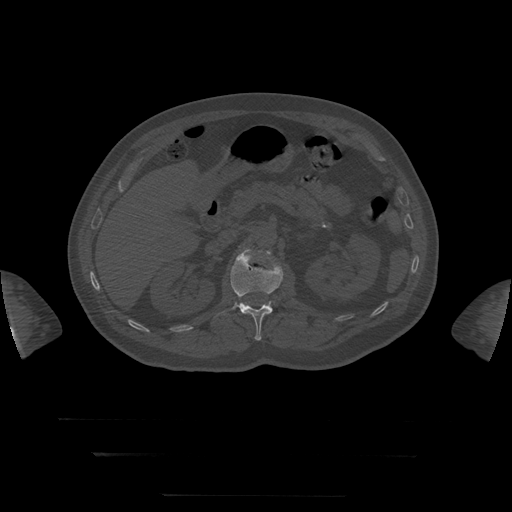
CT including the spine, one axial slice. Reconstruction kernel STANDARD. 120 kVp. Bone window (W 1800 / L 400 HU). 512 × 512 image matrix, field of view 510 × 510 mm. Patient age 73 years. From the clinical record (not read from this slice): primary cancer: prostate.
Structures marked on this image (semi-automatic segmentation, software-assisted and operator-edited):
- L1 vertebra: bounding box (x1, y1, x2, y2) in pixels: (217, 249, 283, 341)